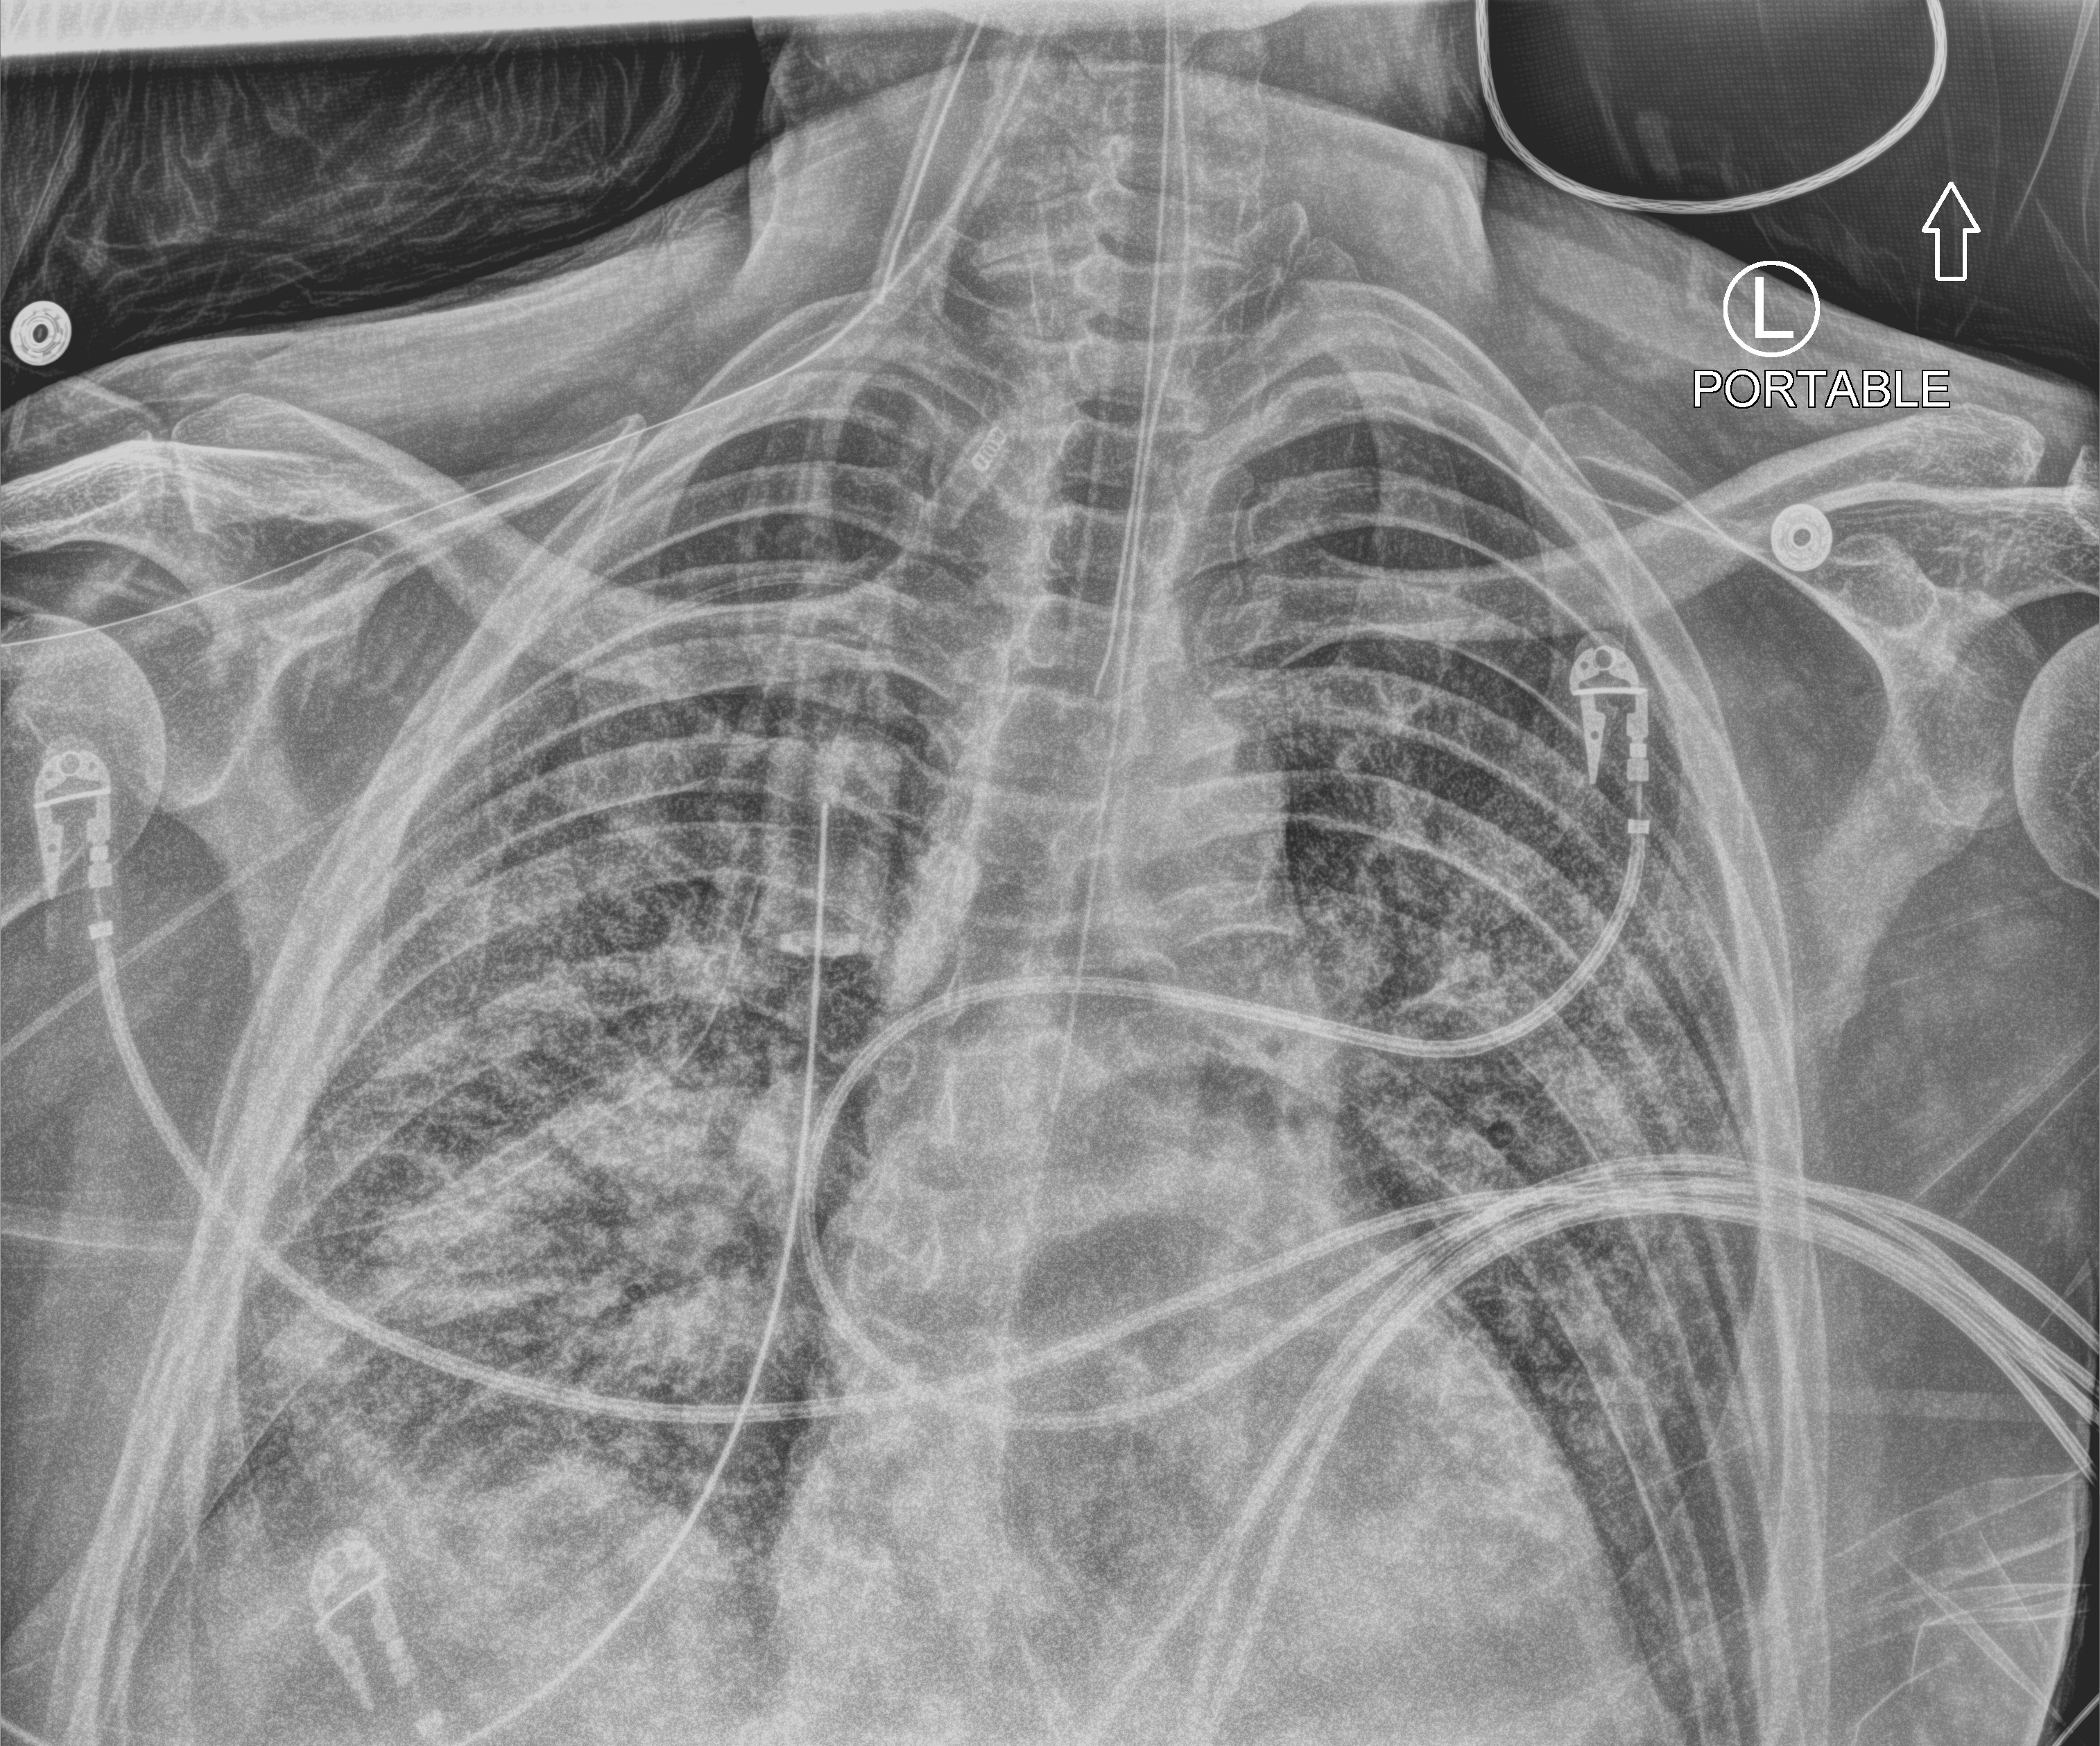
Portable chest radiograph; anteroposterior (AP) projection. Patient hospitalised with COVID-19; male, aged 18–59 years.
Hospital-stay facts (about this admission, not read from this image; timing relative to this image not recorded):
- admitted to intensive care during this hospital stay: yes
- mechanically ventilated during this hospital stay: yes